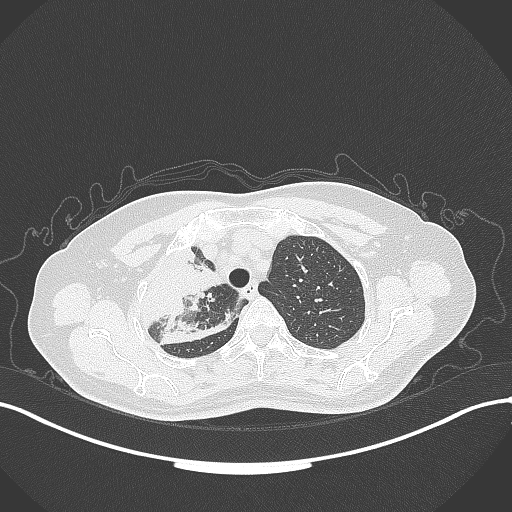
Chest CT, one axial slice. Position 255 of 309 along the scan axis. Reconstruction kernel B70f. 120 kVp. Lung window (W 1500 / L -600 HU). 1 mm slice thickness. 512 × 512 image matrix. Patient: female, 60 years. From the clinical record (not read from this slice): clinical TNM (as recorded): T3 N1 M1.
Structures marked on this image (rectangle marked by the reading radiologist):
- lung tumour (recorded histology: adenocarcinoma): box from (x=131, y=243) to (x=223, y=337) px